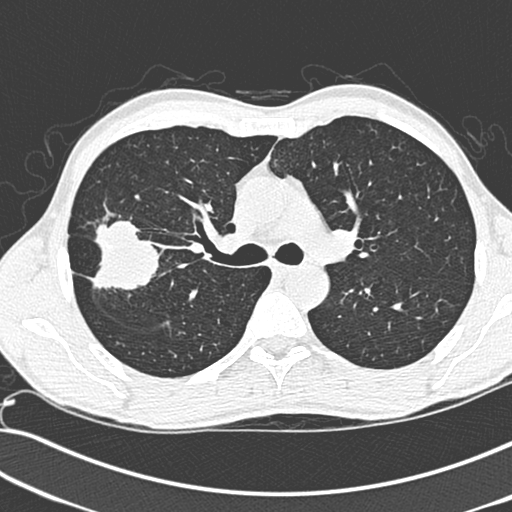
Low-dose screening chest CT, one axial slice; slice 194 of 281 in the series (ordered by position); 120 kVp; lung window (W 1500 / L -600 HU); 512 × 512 image matrix.
Outlined on this slice (expert manual segmentation):
- lesion 1 (tumor, upper lobe of right lung): bounding box <89,218,160,294> (left, top, right, bottom; pixels)